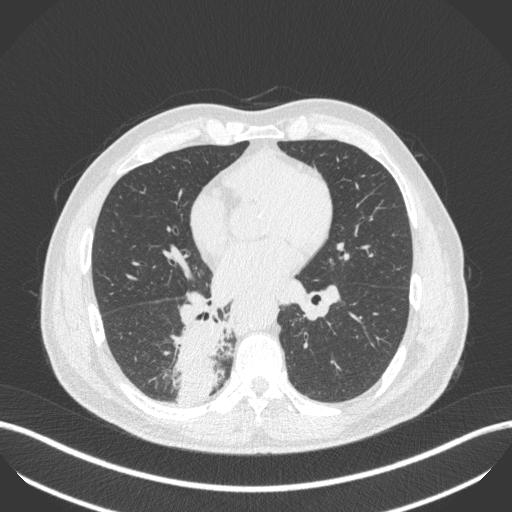
Chest CT, one axial slice. Slice 222 of 451 in the series (ordered by position). 100 kVp. Lung window (W 1500 / L -600 HU). 512 × 512 image matrix, field of view 400 × 400 mm. Male patient, age 61 years. From the clinical record (not read from this slice): clinical TNM (as recorded): T1 N0 M0; histopathological grade: G3.
Annotated regions visible in this slice (bounding box drawn by a radiologist):
- lung tumour (recorded histology: small cell carcinoma): bounding box <167,311,228,411> (left, top, right, bottom; pixels)